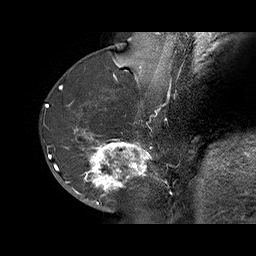
Breast MRI (dynamic contrast-enhanced), one sagittal slice. Position 25 of 70 along the scan axis. Dynamic contrast-enhanced series, time point 2 of 6 at this slice position (early post-contrast). 1.5 T. TE 4.5 ms, TR 32.4 ms. 256 × 256 image matrix, field of view 180 × 180 mm. Female patient. Case-level facts recorded for this patient, not image findings: setting: breast cancer imaged before/during neoadjuvant chemotherapy; receptor status: HR-positive, HER2-negative.
Structures marked on this image (semi-automatically segmented with operator editing):
- analysis volume of interest (the breast-tissue region the enhancement analysis was run in; not a lesion): box from (x=71, y=128) to (x=159, y=202) px
- tumour enhancement mask (voxels above the 100 % enhancement threshold inside the analysis volume of interest): (x=73, y=128)–(x=148, y=202)